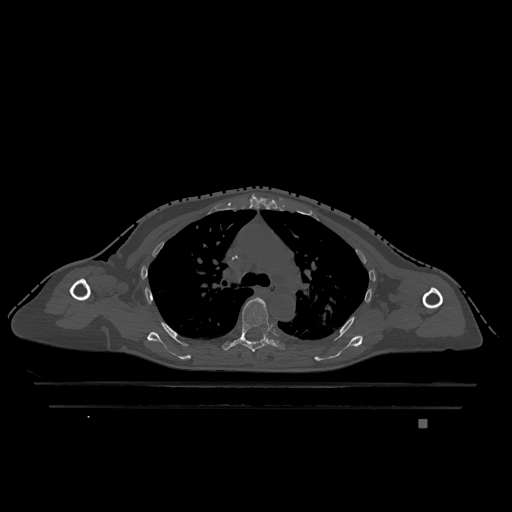
CT including the spine, one axial slice. Bone window (W 1800 / L 400 HU). 0.5 mm slice thickness. 512 × 512 image matrix. Patient: female, 74 years. Case-level facts recorded for this patient, not image findings: primary cancer: lung; vertebrae with lytic lesions (as recorded): T1, T4, T5, T6, L4, L5.
Outlined on this slice (semi-automatic segmentation, software-assisted and operator-edited):
- T5 vertebra: bounding box [x1, y1, x2, y2] px = [222, 298, 286, 352]